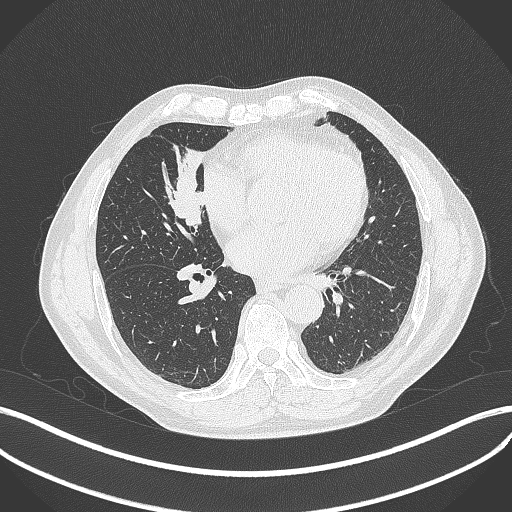
Chest CT, one axial slice. Slice 171 of 429 in the series (ordered by position). Reconstruction kernel B70f. Lung window (W 1500 / L -600 HU). 1 mm slice thickness. 512 × 512 image matrix, field of view 400 × 400 mm. Male patient, age 61 years. From the clinical record (not read from this slice): clinical TNM (as recorded): T2b N1 M0.
Outlined on this slice (rectangle marked by the reading radiologist):
- lung tumour (recorded histology: squamous cell carcinoma): box from (x=155, y=143) to (x=207, y=236) px